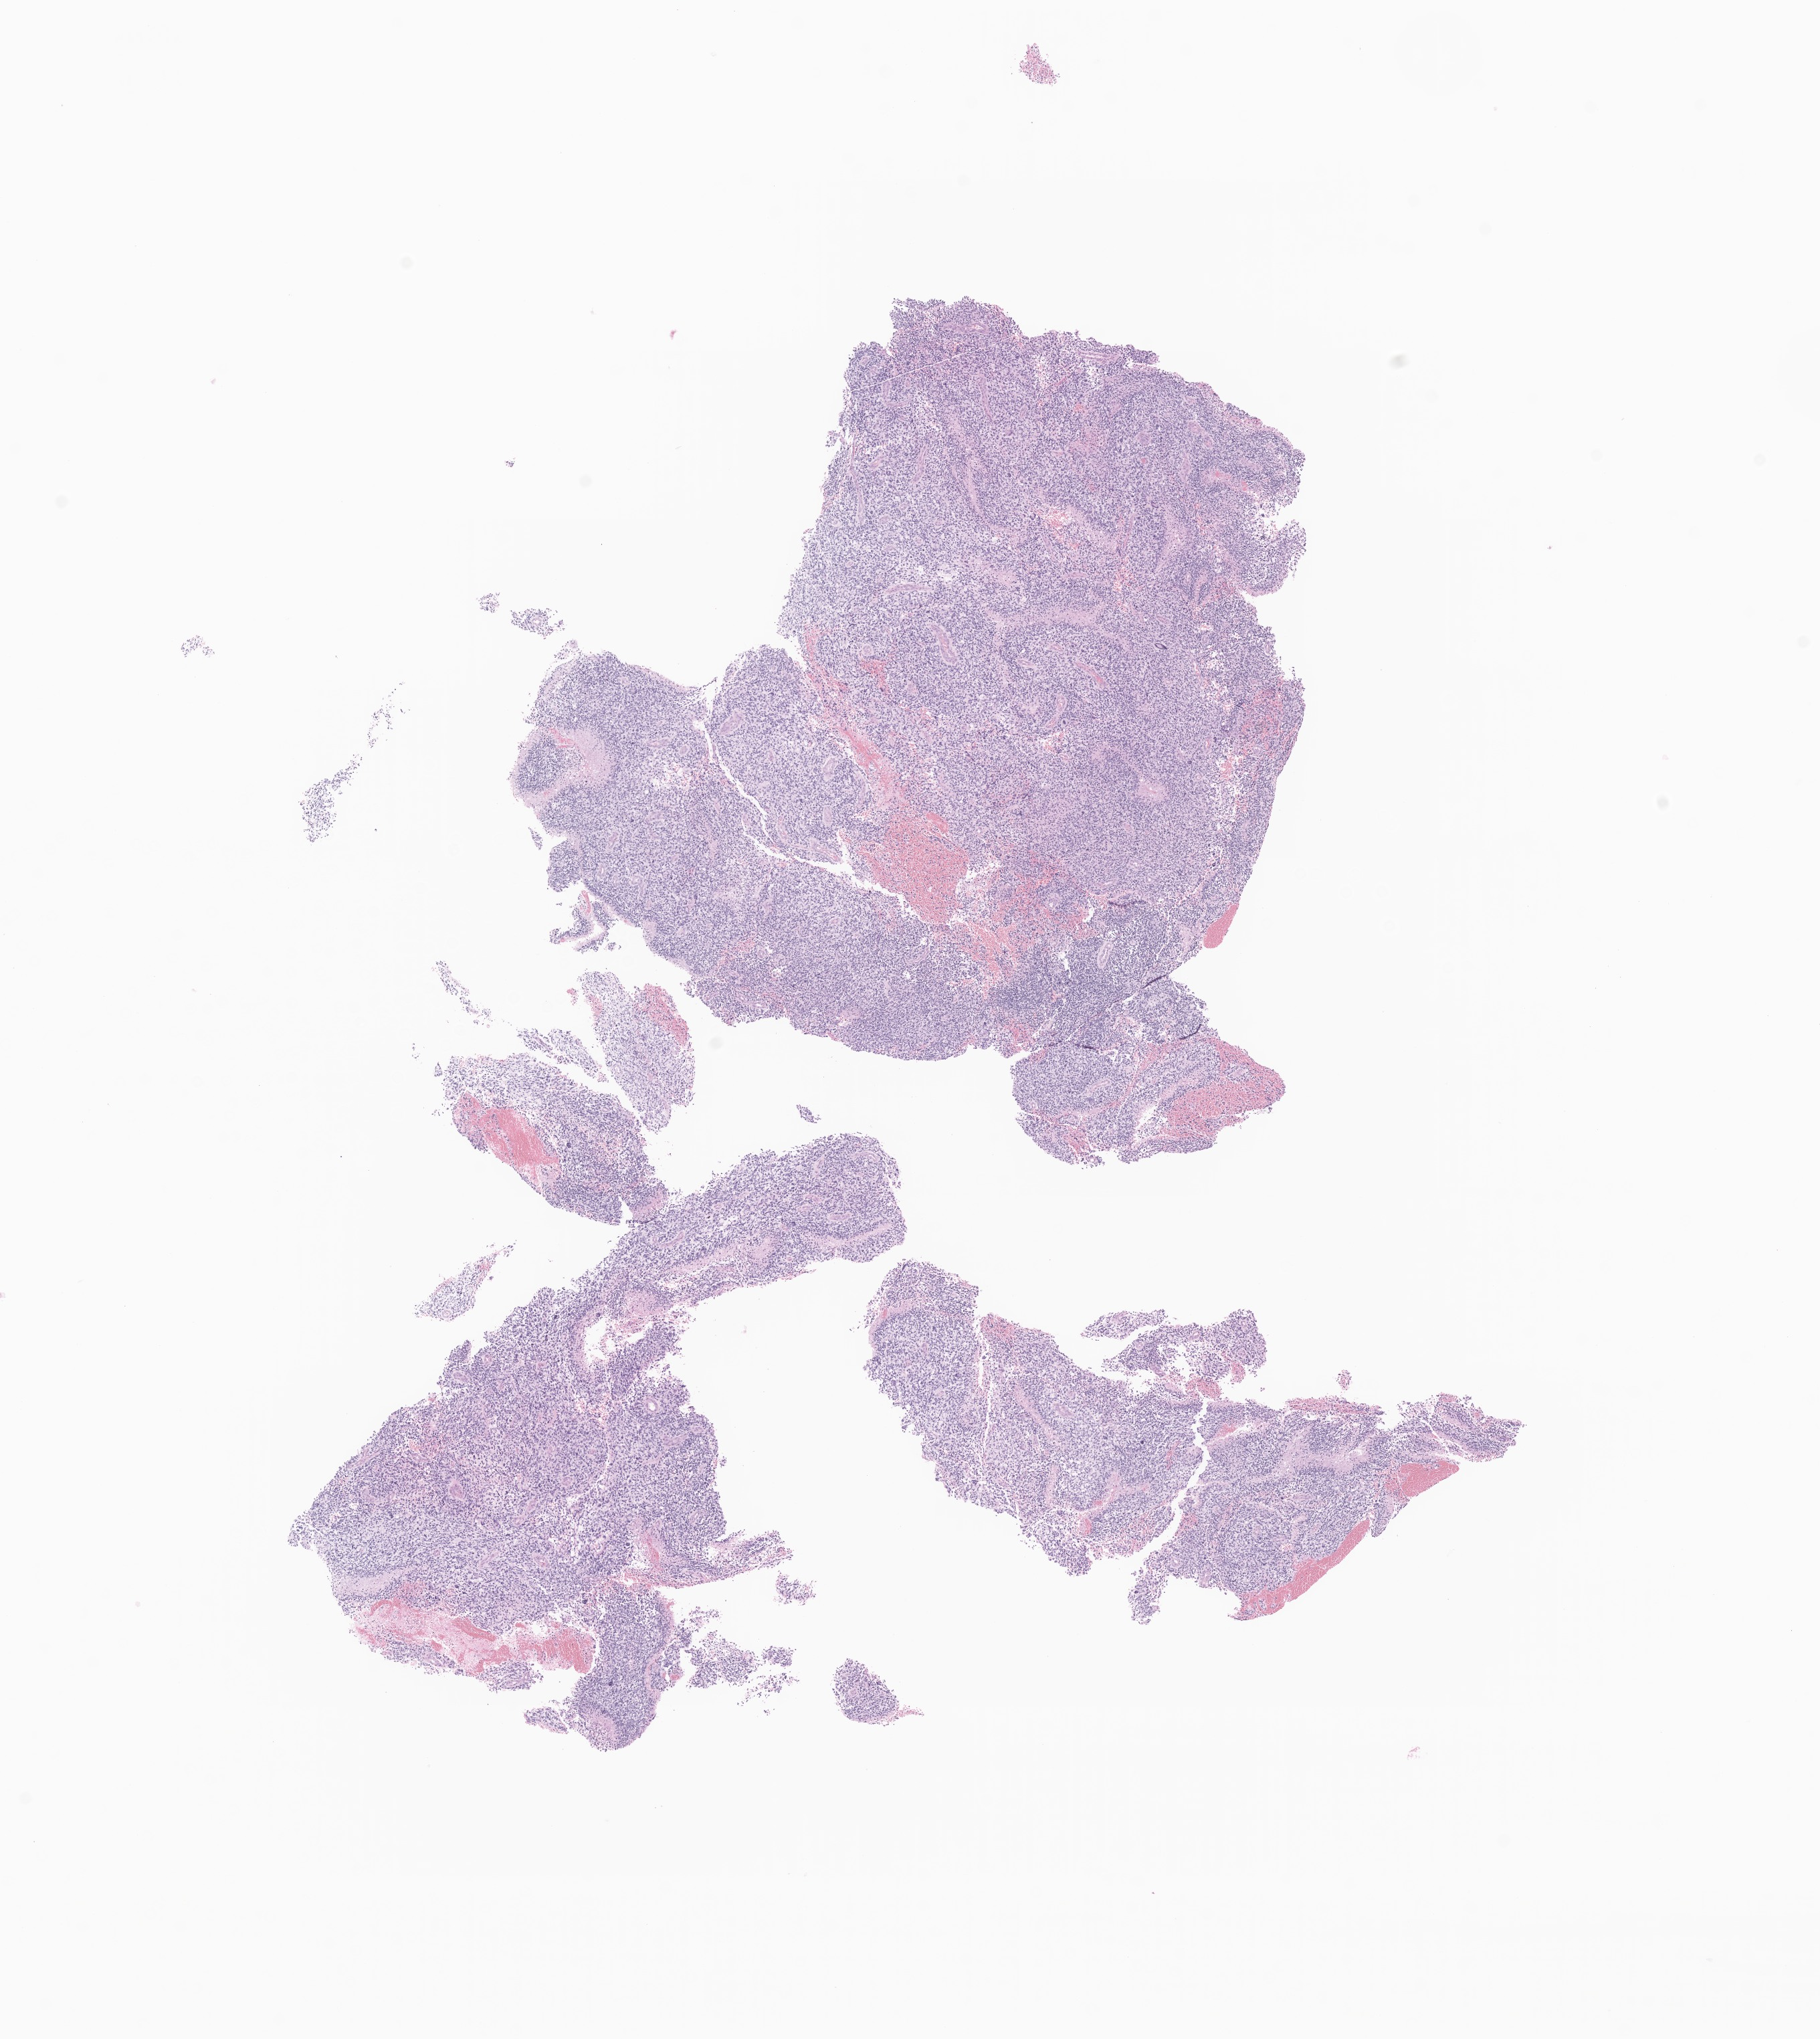
Whole-slide image, haematoxylin and eosin stain of tumor tissue from the brain — whole scanned area (about 11.5 x 12.9 mm) shown as a low-resolution overview, FFPE section. Patient male; age 144 months (12 years).
- recorded diagnosis: Glioma, malignant